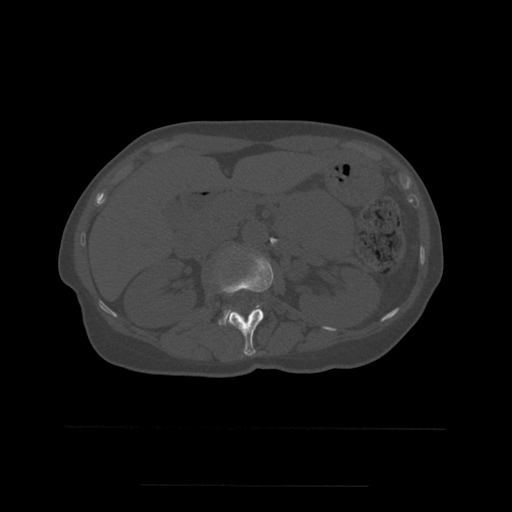
CT including the spine, one axial slice. Position 227 of 544 along the scan axis. Bone window (W 1800 / L 400 HU). 1.25 mm slice thickness. 512 × 512 image matrix, field of view 350 × 350 mm. Patient age 58 years. Case-level facts recorded for this patient, not image findings: primary cancer: lung.
Structures marked on this image (semi-automatically segmented with operator editing):
- L1 vertebra: bounding box [x1, y1, x2, y2] px = [220, 254, 274, 356]
- L2 vertebra: [219, 310, 231, 326]